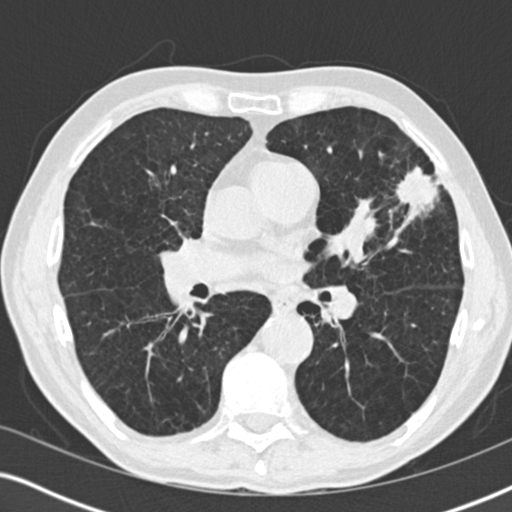
Low-dose screening chest CT, one axial slice; position 101 of 196 along the scan axis; reconstruction kernel B30f; 120 kVp; lung window (W 1500 / L -600 HU); 2 mm slice thickness; 512 × 512 image matrix.
Structures marked on this image (expert manual segmentation):
- lesion 1 (tumor, upper lobe of left lung): bounding box [x1, y1, x2, y2] px = [397, 167, 438, 206]